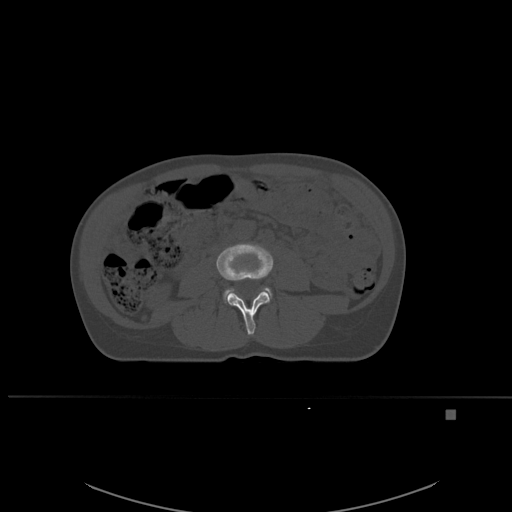
CT including the spine, one axial slice. Slice 206 of 537 in the series (ordered by position). Bone window (W 1800 / L 400 HU). 1.5 mm slice thickness. 512 × 512 image matrix, field of view 440 × 440 mm. Female patient, age 45 years. Case-level facts recorded for this patient, not image findings: primary cancer: lung.
Outlined on this slice (semi-automatically segmented with operator editing):
- L3 vertebra: bounding box (x1, y1, x2, y2) in pixels: (216, 243, 274, 335)
- L4 vertebra: (224, 288, 270, 303)